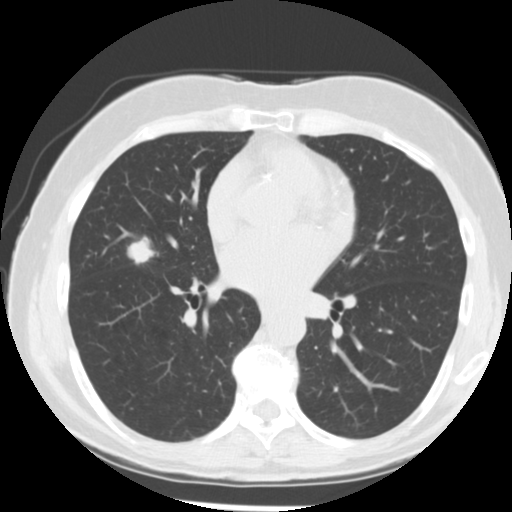
Low-dose screening chest CT, one axial slice. Position 134 of 255 along the scan axis. Lung window (W 1500 / L -600 HU). 512 × 512 image matrix, field of view 320 × 320 mm.
Outlined on this slice (expert manual segmentation):
- lesion 1 (tumor, middle lobe of right lung): bounding box (x1, y1, x2, y2) in pixels: (127, 240, 155, 264)